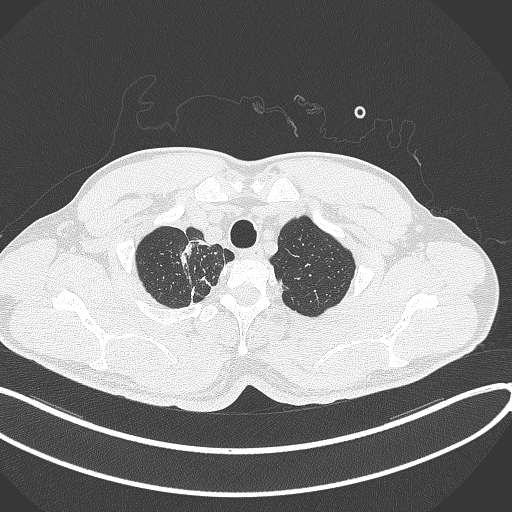
Chest CT, one axial slice; slice 338 of 391 in the series (ordered by position); lung window (W 1500 / L -600 HU); 1 mm slice thickness; 512 × 512 image matrix. Male patient, age 48 years. Case-level facts recorded for this patient, not image findings: clinical TNM (as recorded): T1c N1 M1.
Annotated regions visible in this slice (rectangle marked by the reading radiologist):
- lung tumour (recorded histology: adenocarcinoma): bounding box (x1, y1, x2, y2) in pixels: (176, 241, 199, 268)